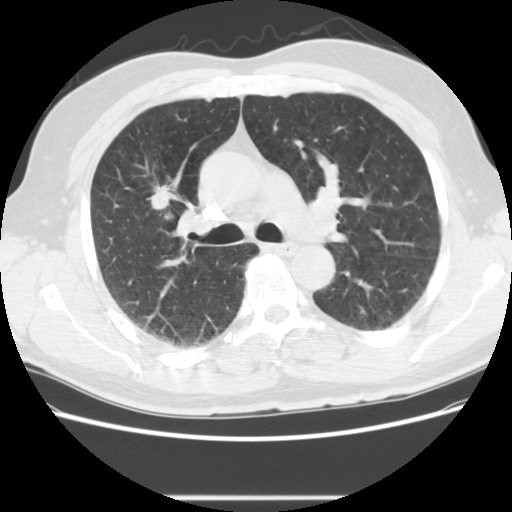
Low-dose screening chest CT, axial slice. Second screening round (one year after baseline). Lung window (W 1500 / L -600 HU). 2.5 mm slice thickness. Slice 53 of 139 in the series. Male participant, aged 59 years at enrolment. Current smoker at enrolment.
• Expert-annotated lung lesion, bounding box [x1, y1, x2, y2] px = [138, 178, 178, 218].
• Reader record for this screening exam (exam-level; its link to the box is not recorded): non-calcified nodule or mass ≥4 mm, right upper lobe, 20 × 13 mm, spiculated (stellate) margins, soft tissue attenuation, pre-existing on the prior screen: yes; interval growth: yes.